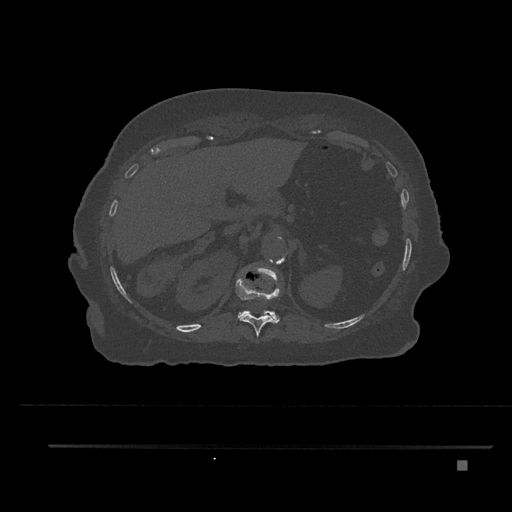
CT including the spine, one axial slice. Slice 297 of 797 in the series (ordered by position). Reconstruction kernel Br40s/3. Bone window (W 1800 / L 400 HU). 512 × 512 image matrix, field of view 437 × 437 mm. Female patient, age 76 years. Case-level facts recorded for this patient, not image findings: primary cancer: lung; vertebrae with lytic lesions (as recorded): T11, L3.
Structures marked on this image (semi-automatic segmentation, software-assisted and operator-edited):
- T11 vertebra: bounding box <235,274,282,336> (left, top, right, bottom; pixels)
- T12 vertebra: <238,268,280,323>